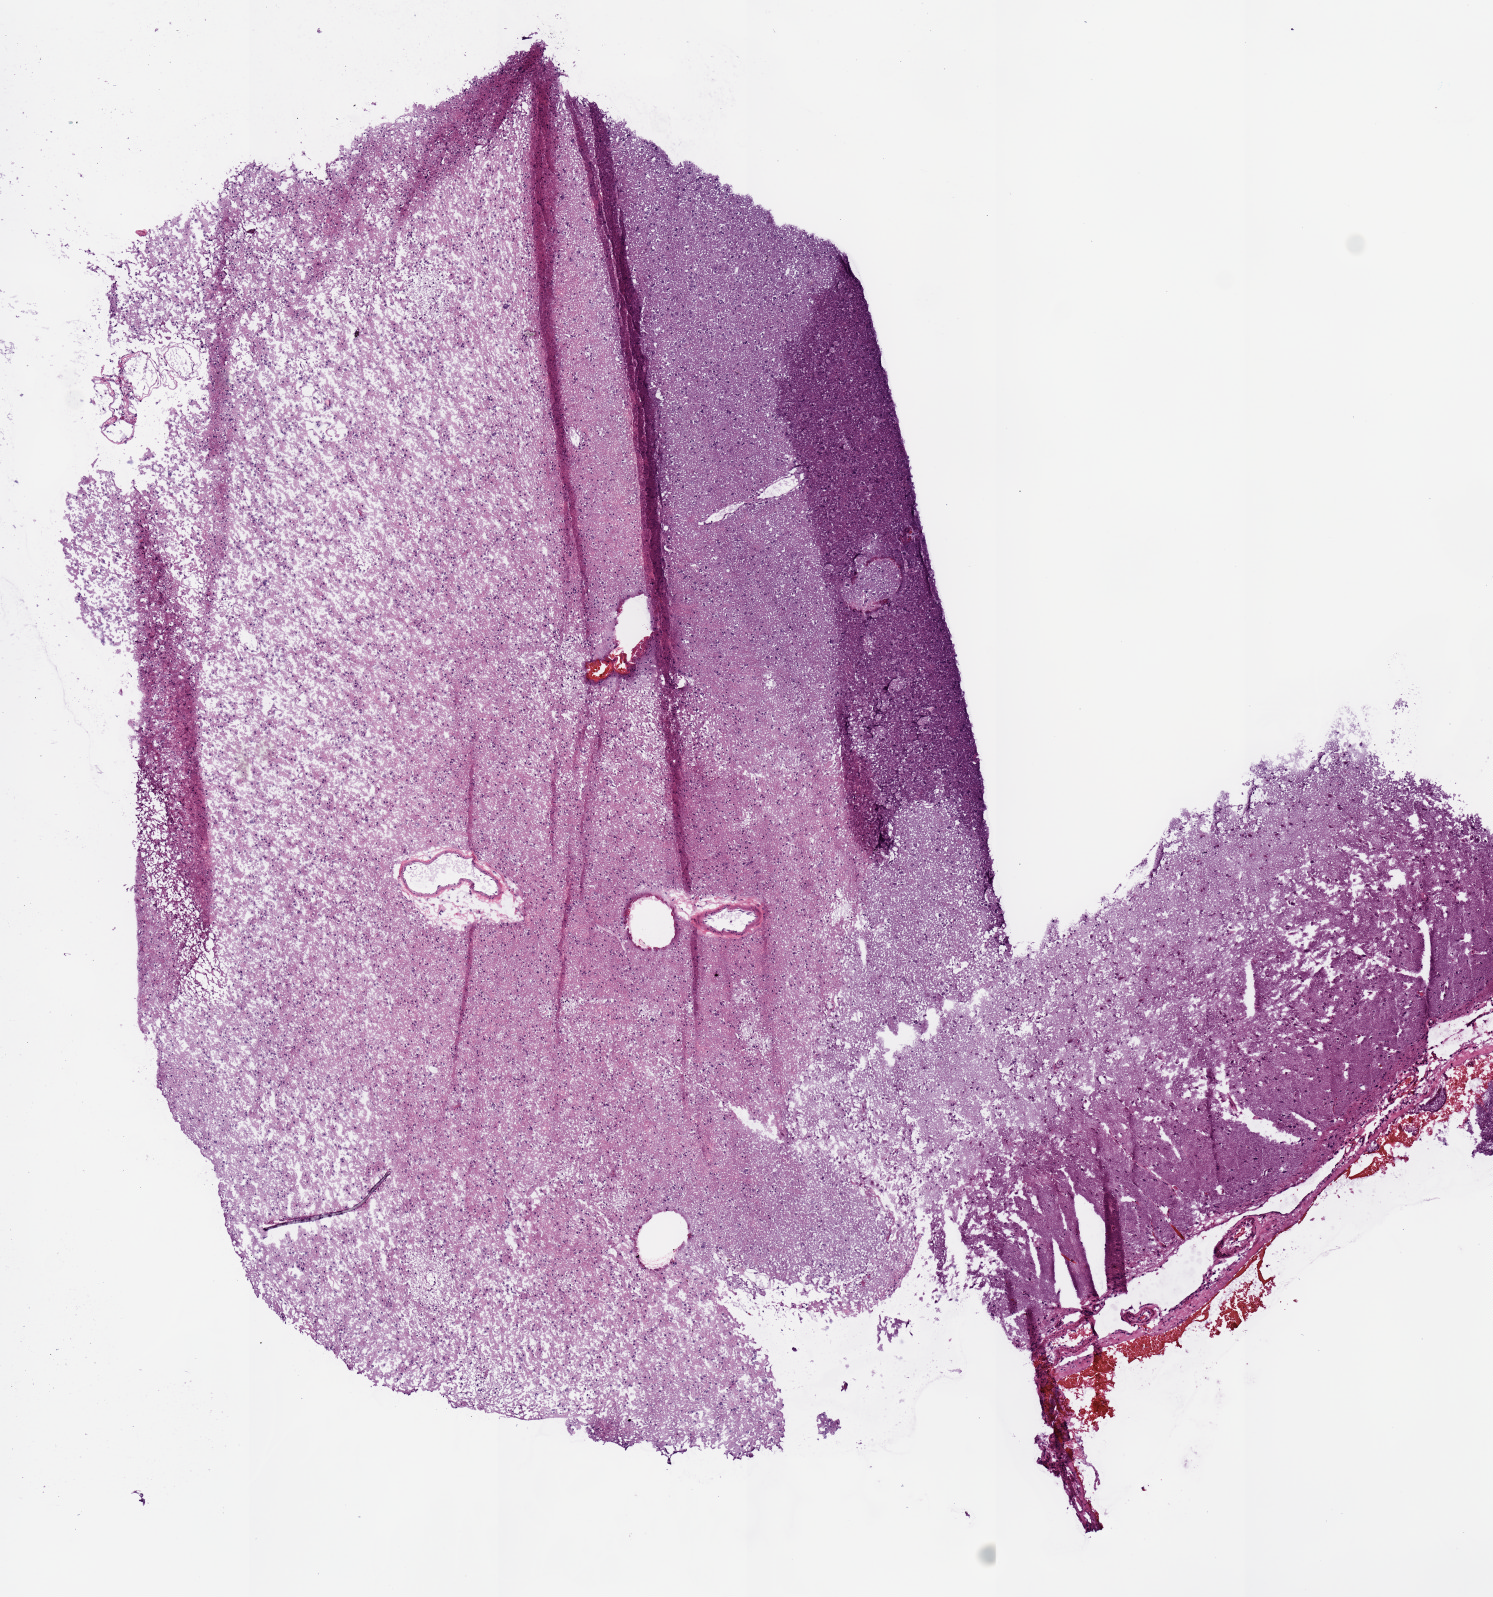
H&E whole-slide image, shown as a low-resolution overview of the whole scanned area (about 5.9 x 6.3 mm, acquisition: 20x scan); frozen section from the bottom of the tissue portion; primary tumour sample from the brain. Patient: female, age at initial diagnosis 49 years. Histologic grade: G2 (moderately differentiated). Slide review estimates, as recorded: tumour nuclei 60%, necrosis 0%.
Diagnosis: Mixed glioma (cerebrum).